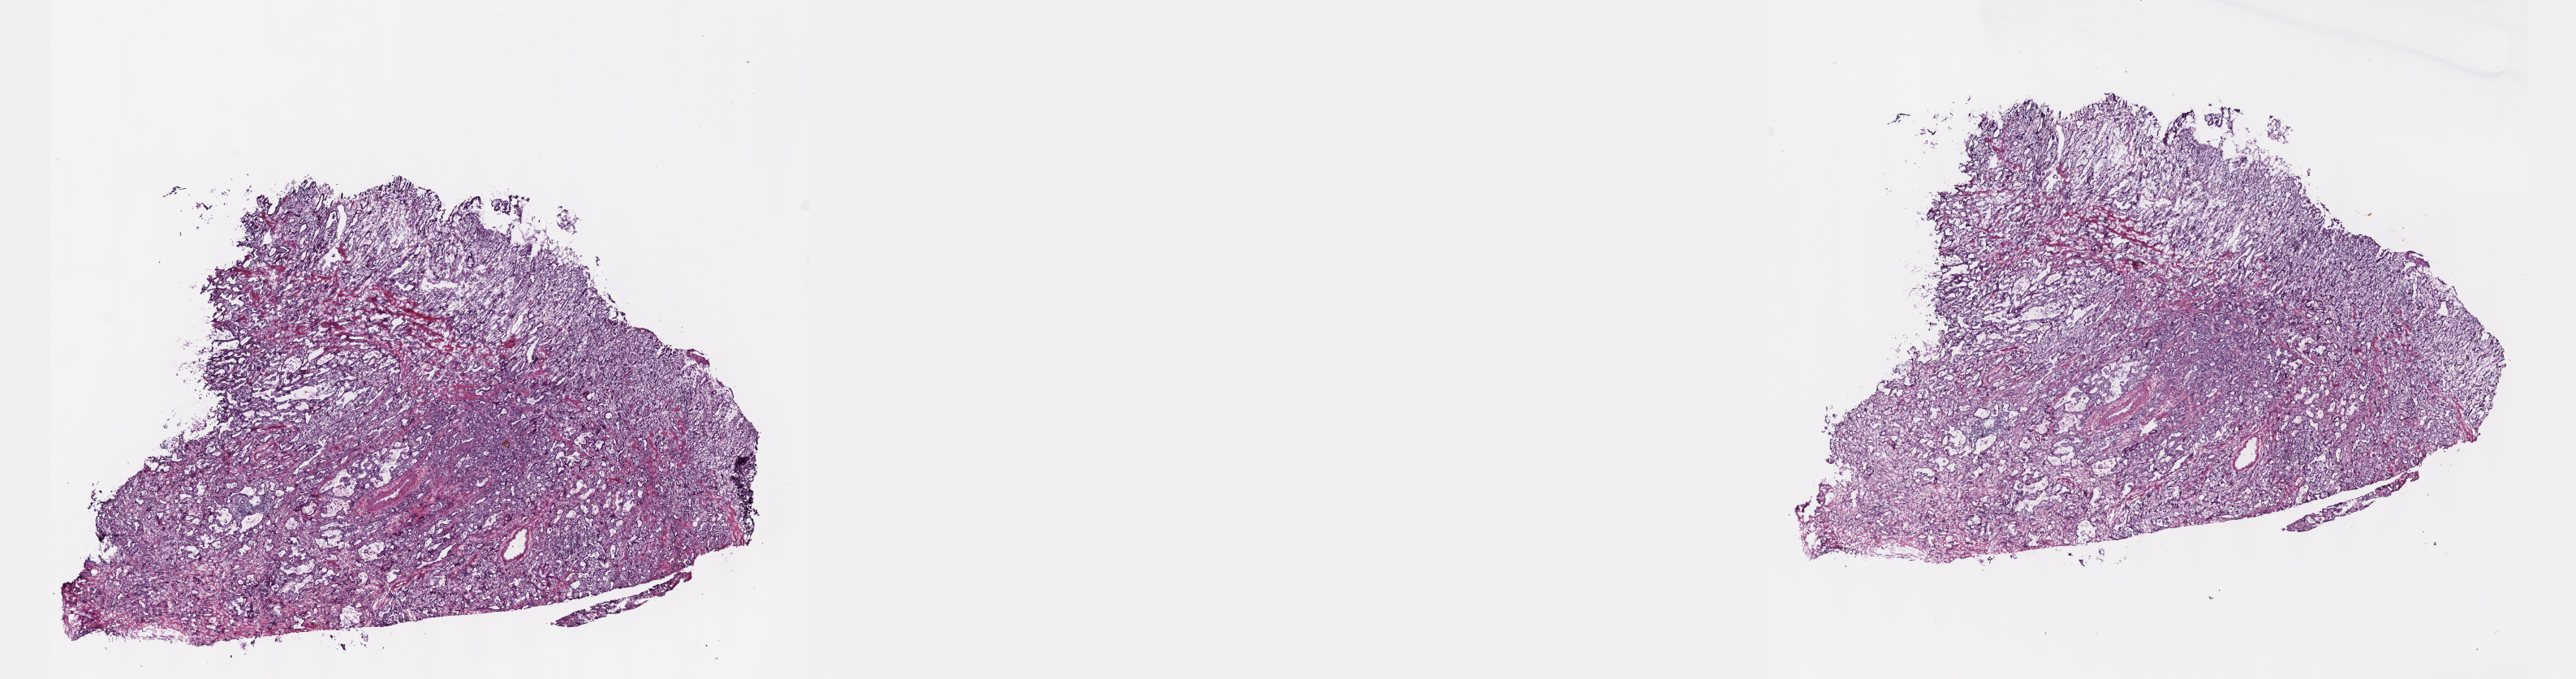
Hematoxylin and eosin (H&E) stained whole-slide image, whole scanned area (about 25.7 x 6.8 mm, slide scanned at 40x) shown as a low-resolution overview. Frozen section from the top of the tissue portion. Sample: primary tumour, esophagus. Patient: male, age at initial diagnosis 75 years. Histologic grade: G3 (poorly differentiated). Pathologist review of this section (percent, as recorded): tumour cells 100%, tumour nuclei 70%, normal cells 0%, stromal cells 0%, necrosis 0%. Infiltration values recorded for this section: lymphocyte infiltration 4%, monocyte infiltration 0%, neutrophil infiltration 0%.
• pathologic diagnosis: Adenocarcinoma, NOS (lower third of esophagus)
• AJCC pathologic stage: IIA
• lymph nodes positive (case pathology): 0 of 4 examined